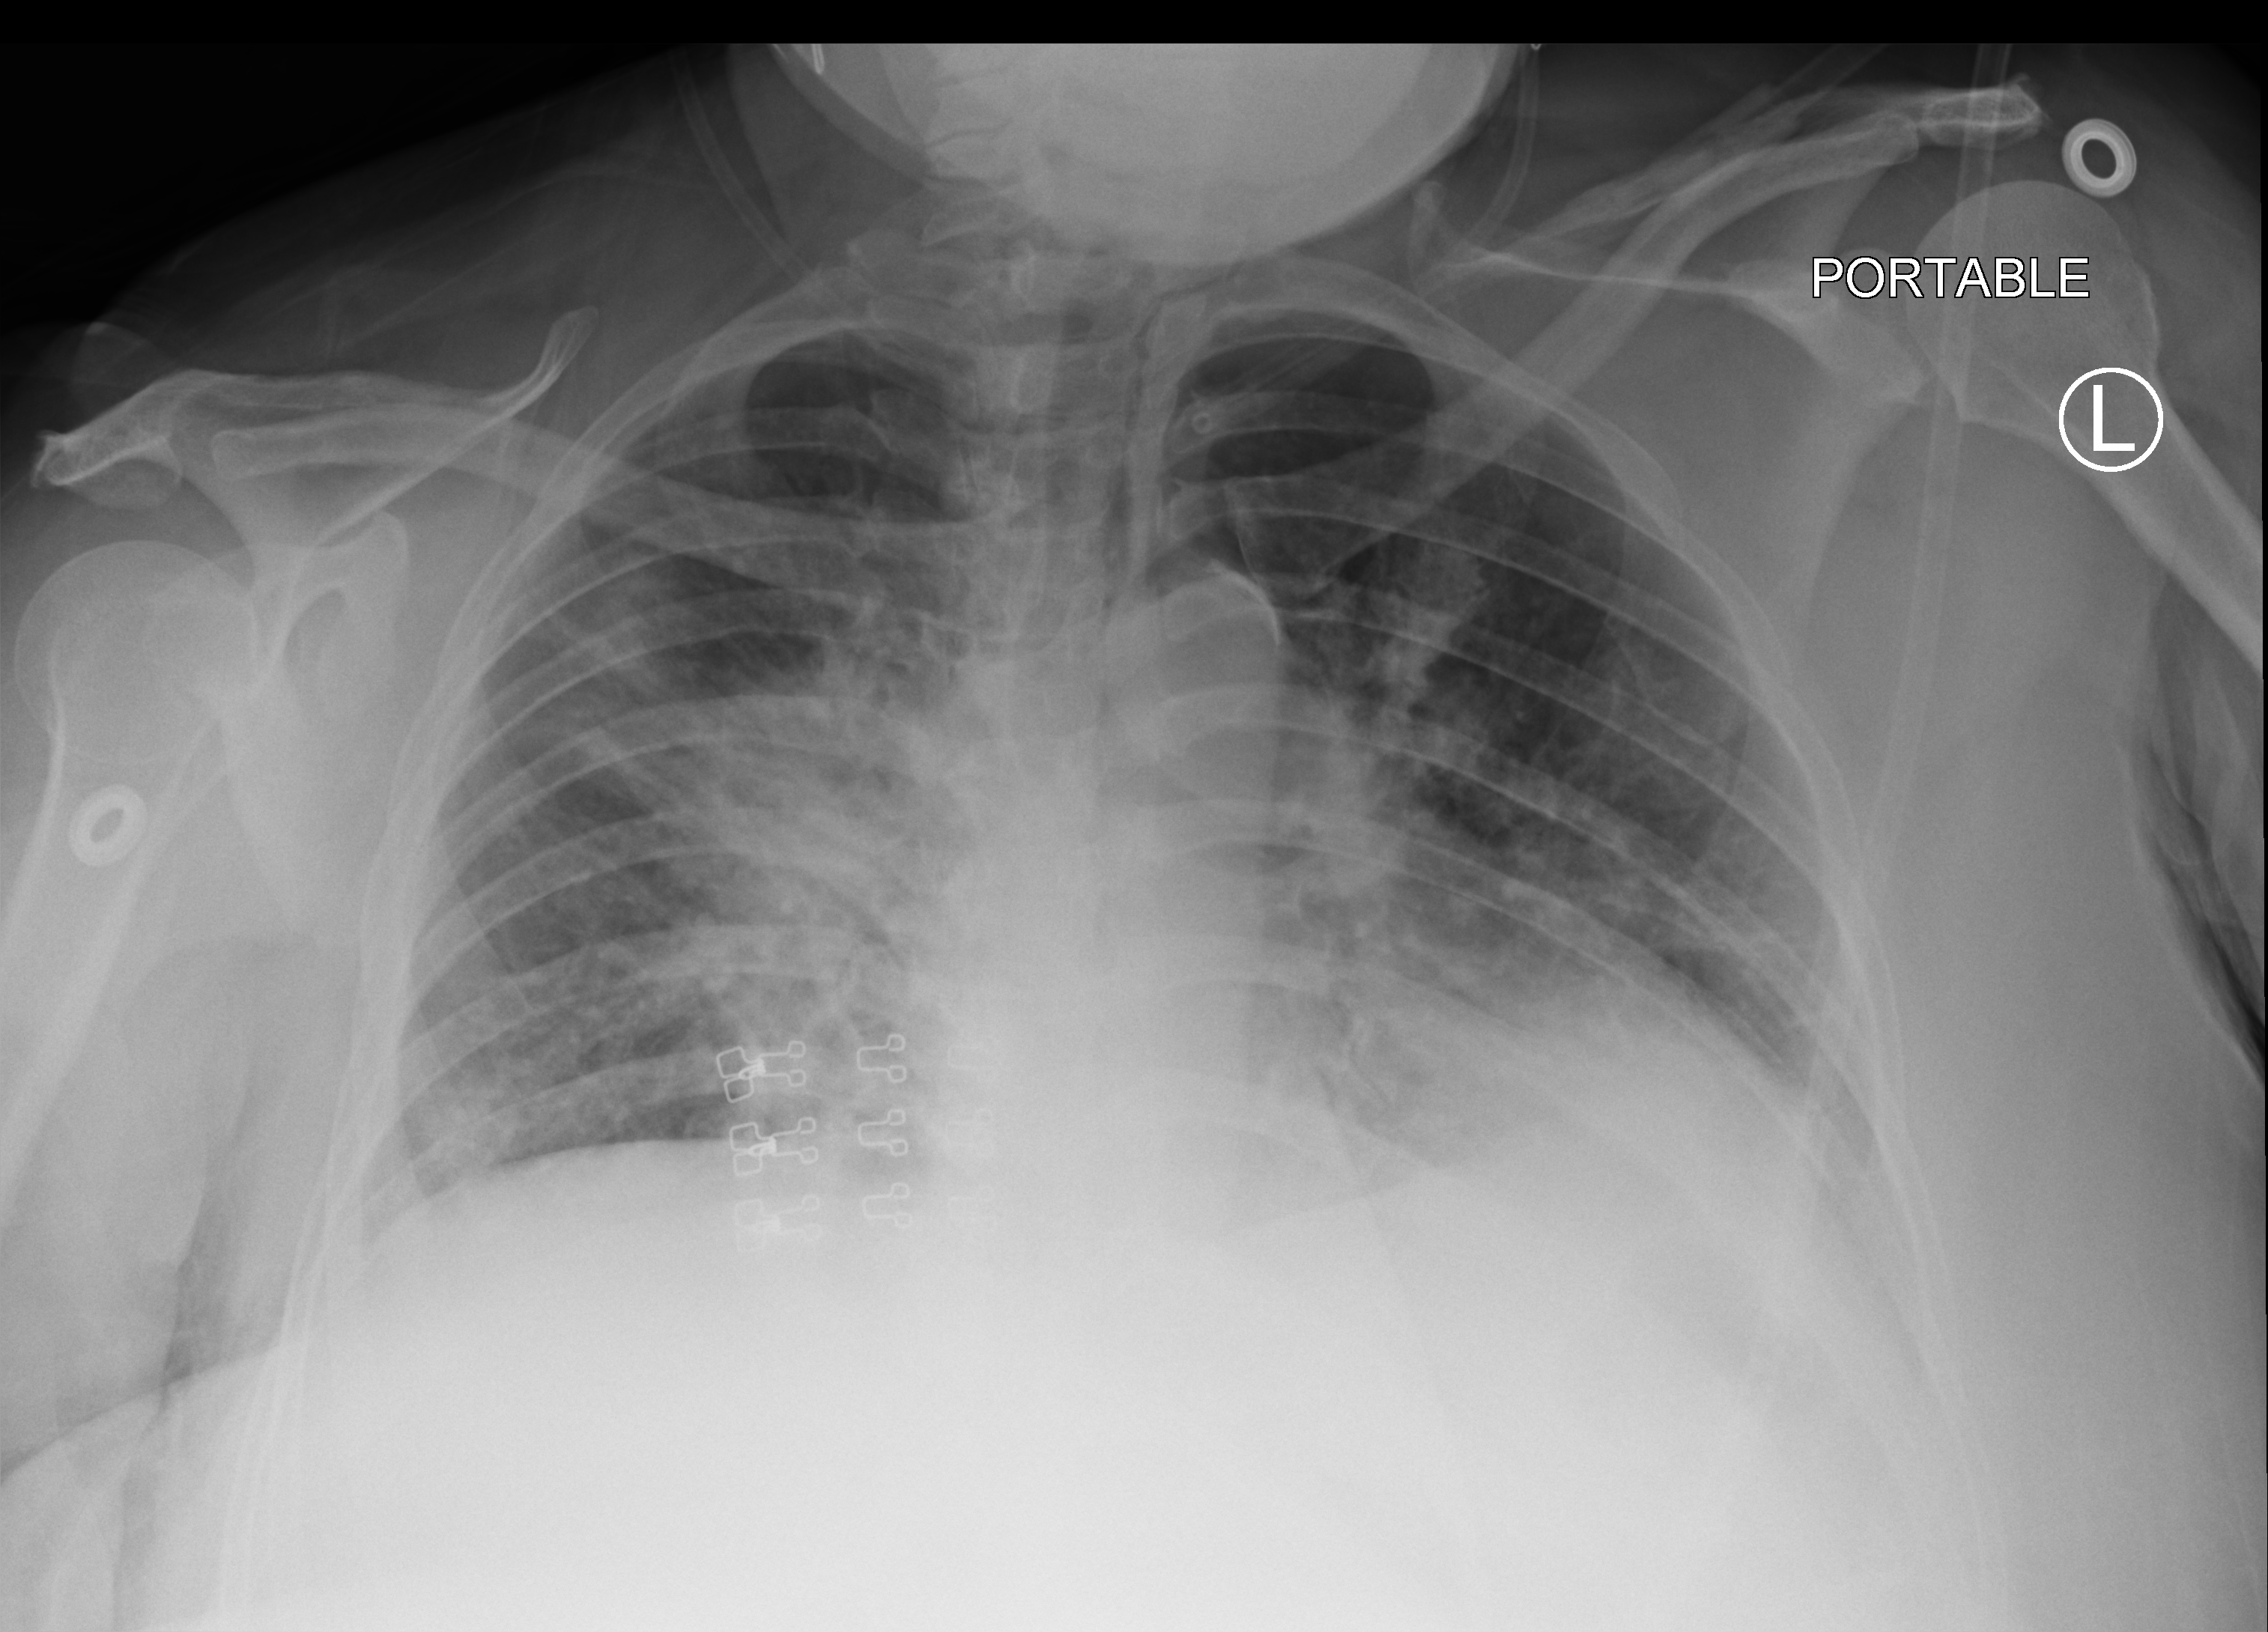
Bedside chest radiograph (computed radiography). Patient hospitalised with COVID-19; female, aged 18–59 years.
Admission-level facts for this patient (not findings on this image; timing relative to this image not recorded): hypertension (admission record): yes; mechanically ventilated during this hospital stay: no; admitted to intensive care during this hospital stay: no.